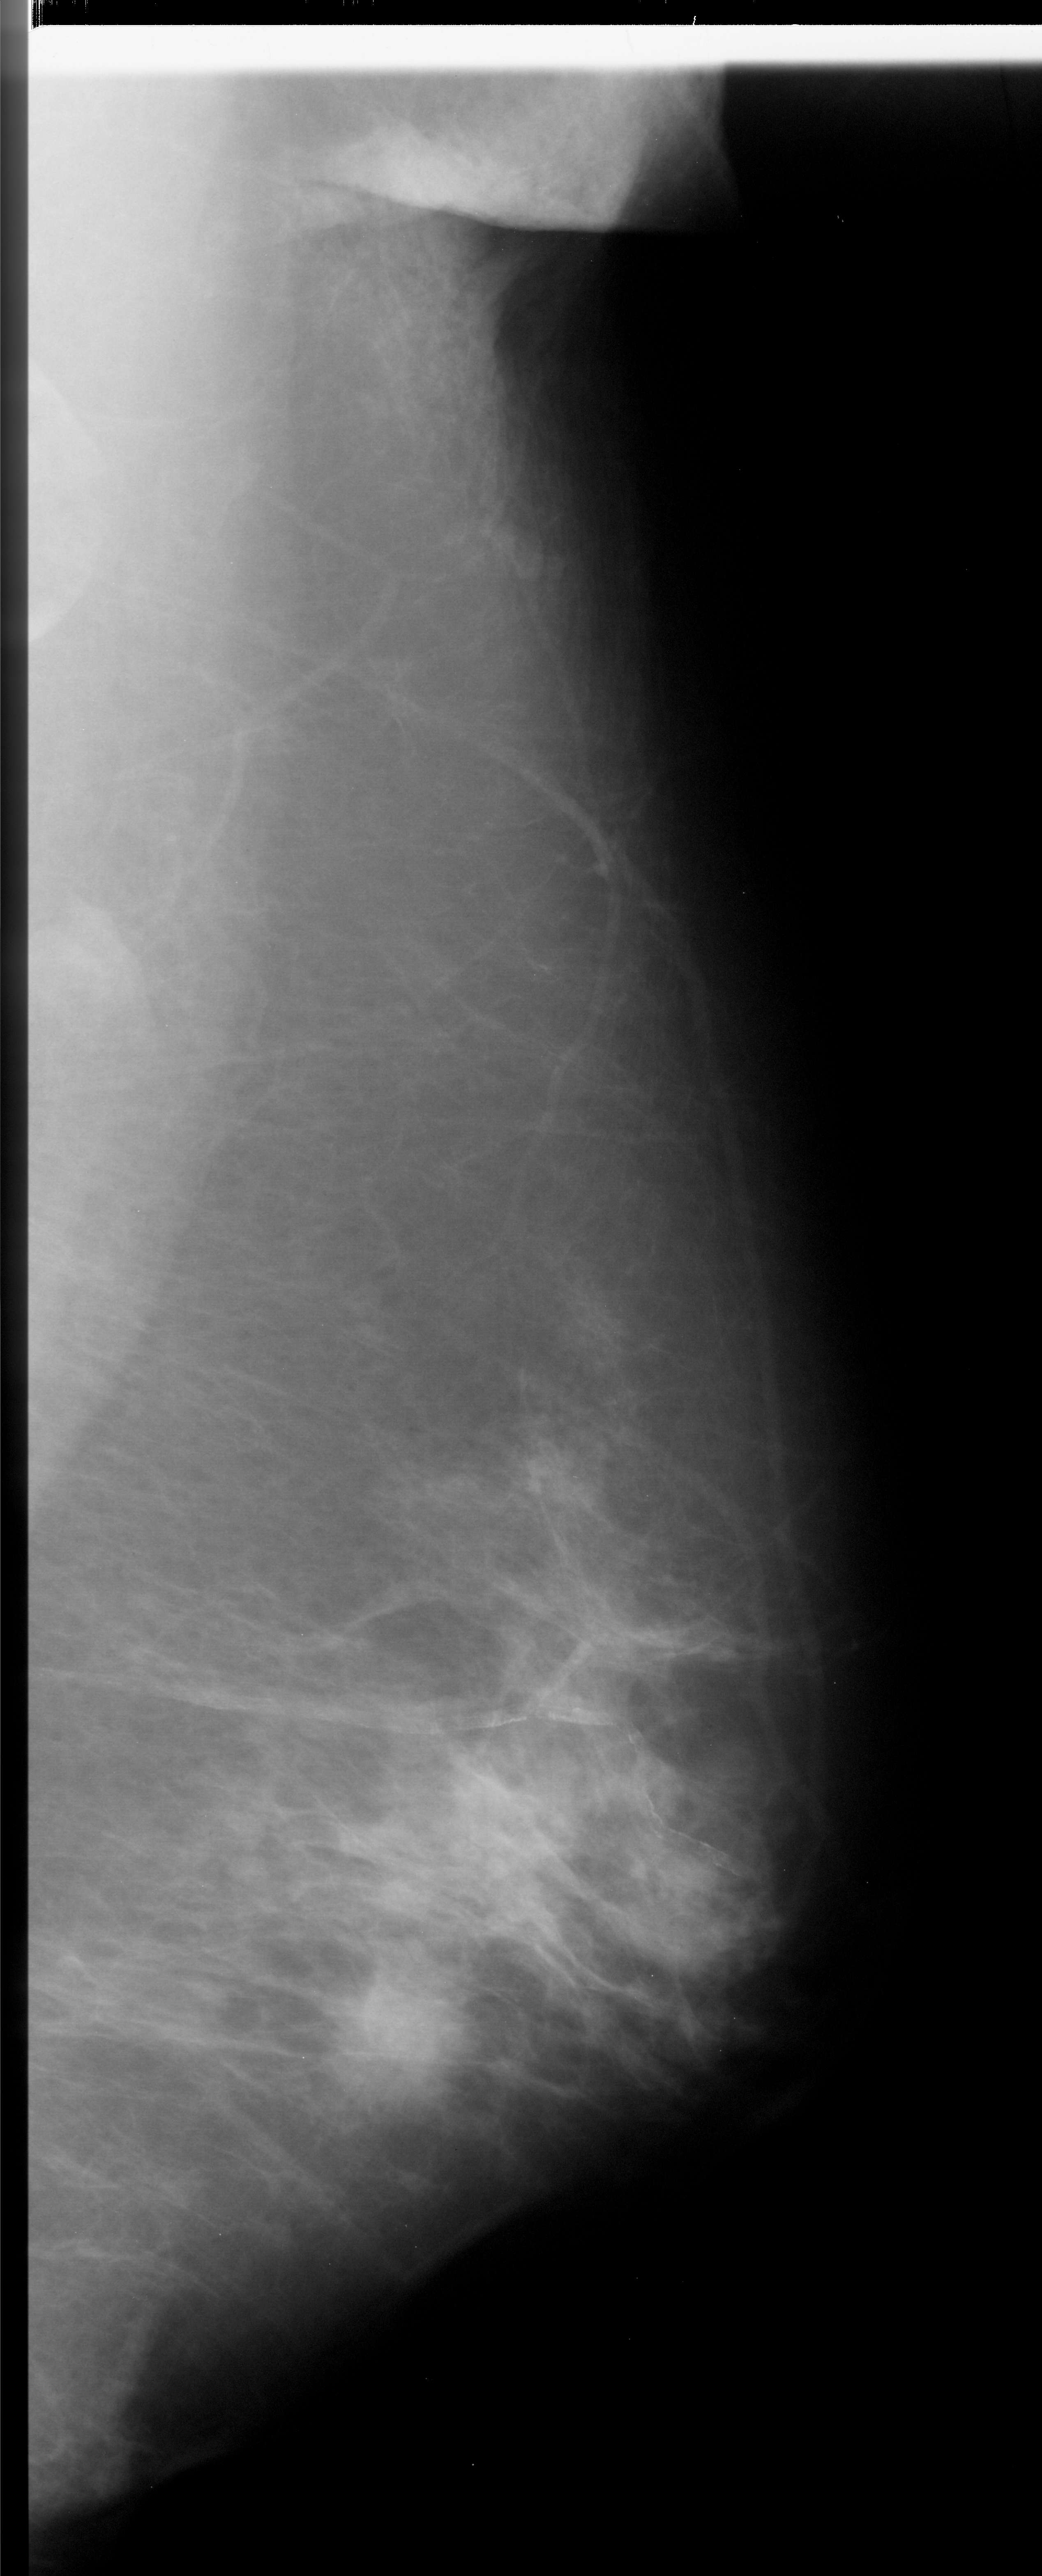
Mammogram (digitized film), right breast, mediolateral oblique (MLO) view.
- Marked findings (only marked abnormalities are described; nothing is implied about the rest of the image): mass, shape irregular, margins spiculated; BI-RADS assessment category 5; pathology (as recorded): malignant.